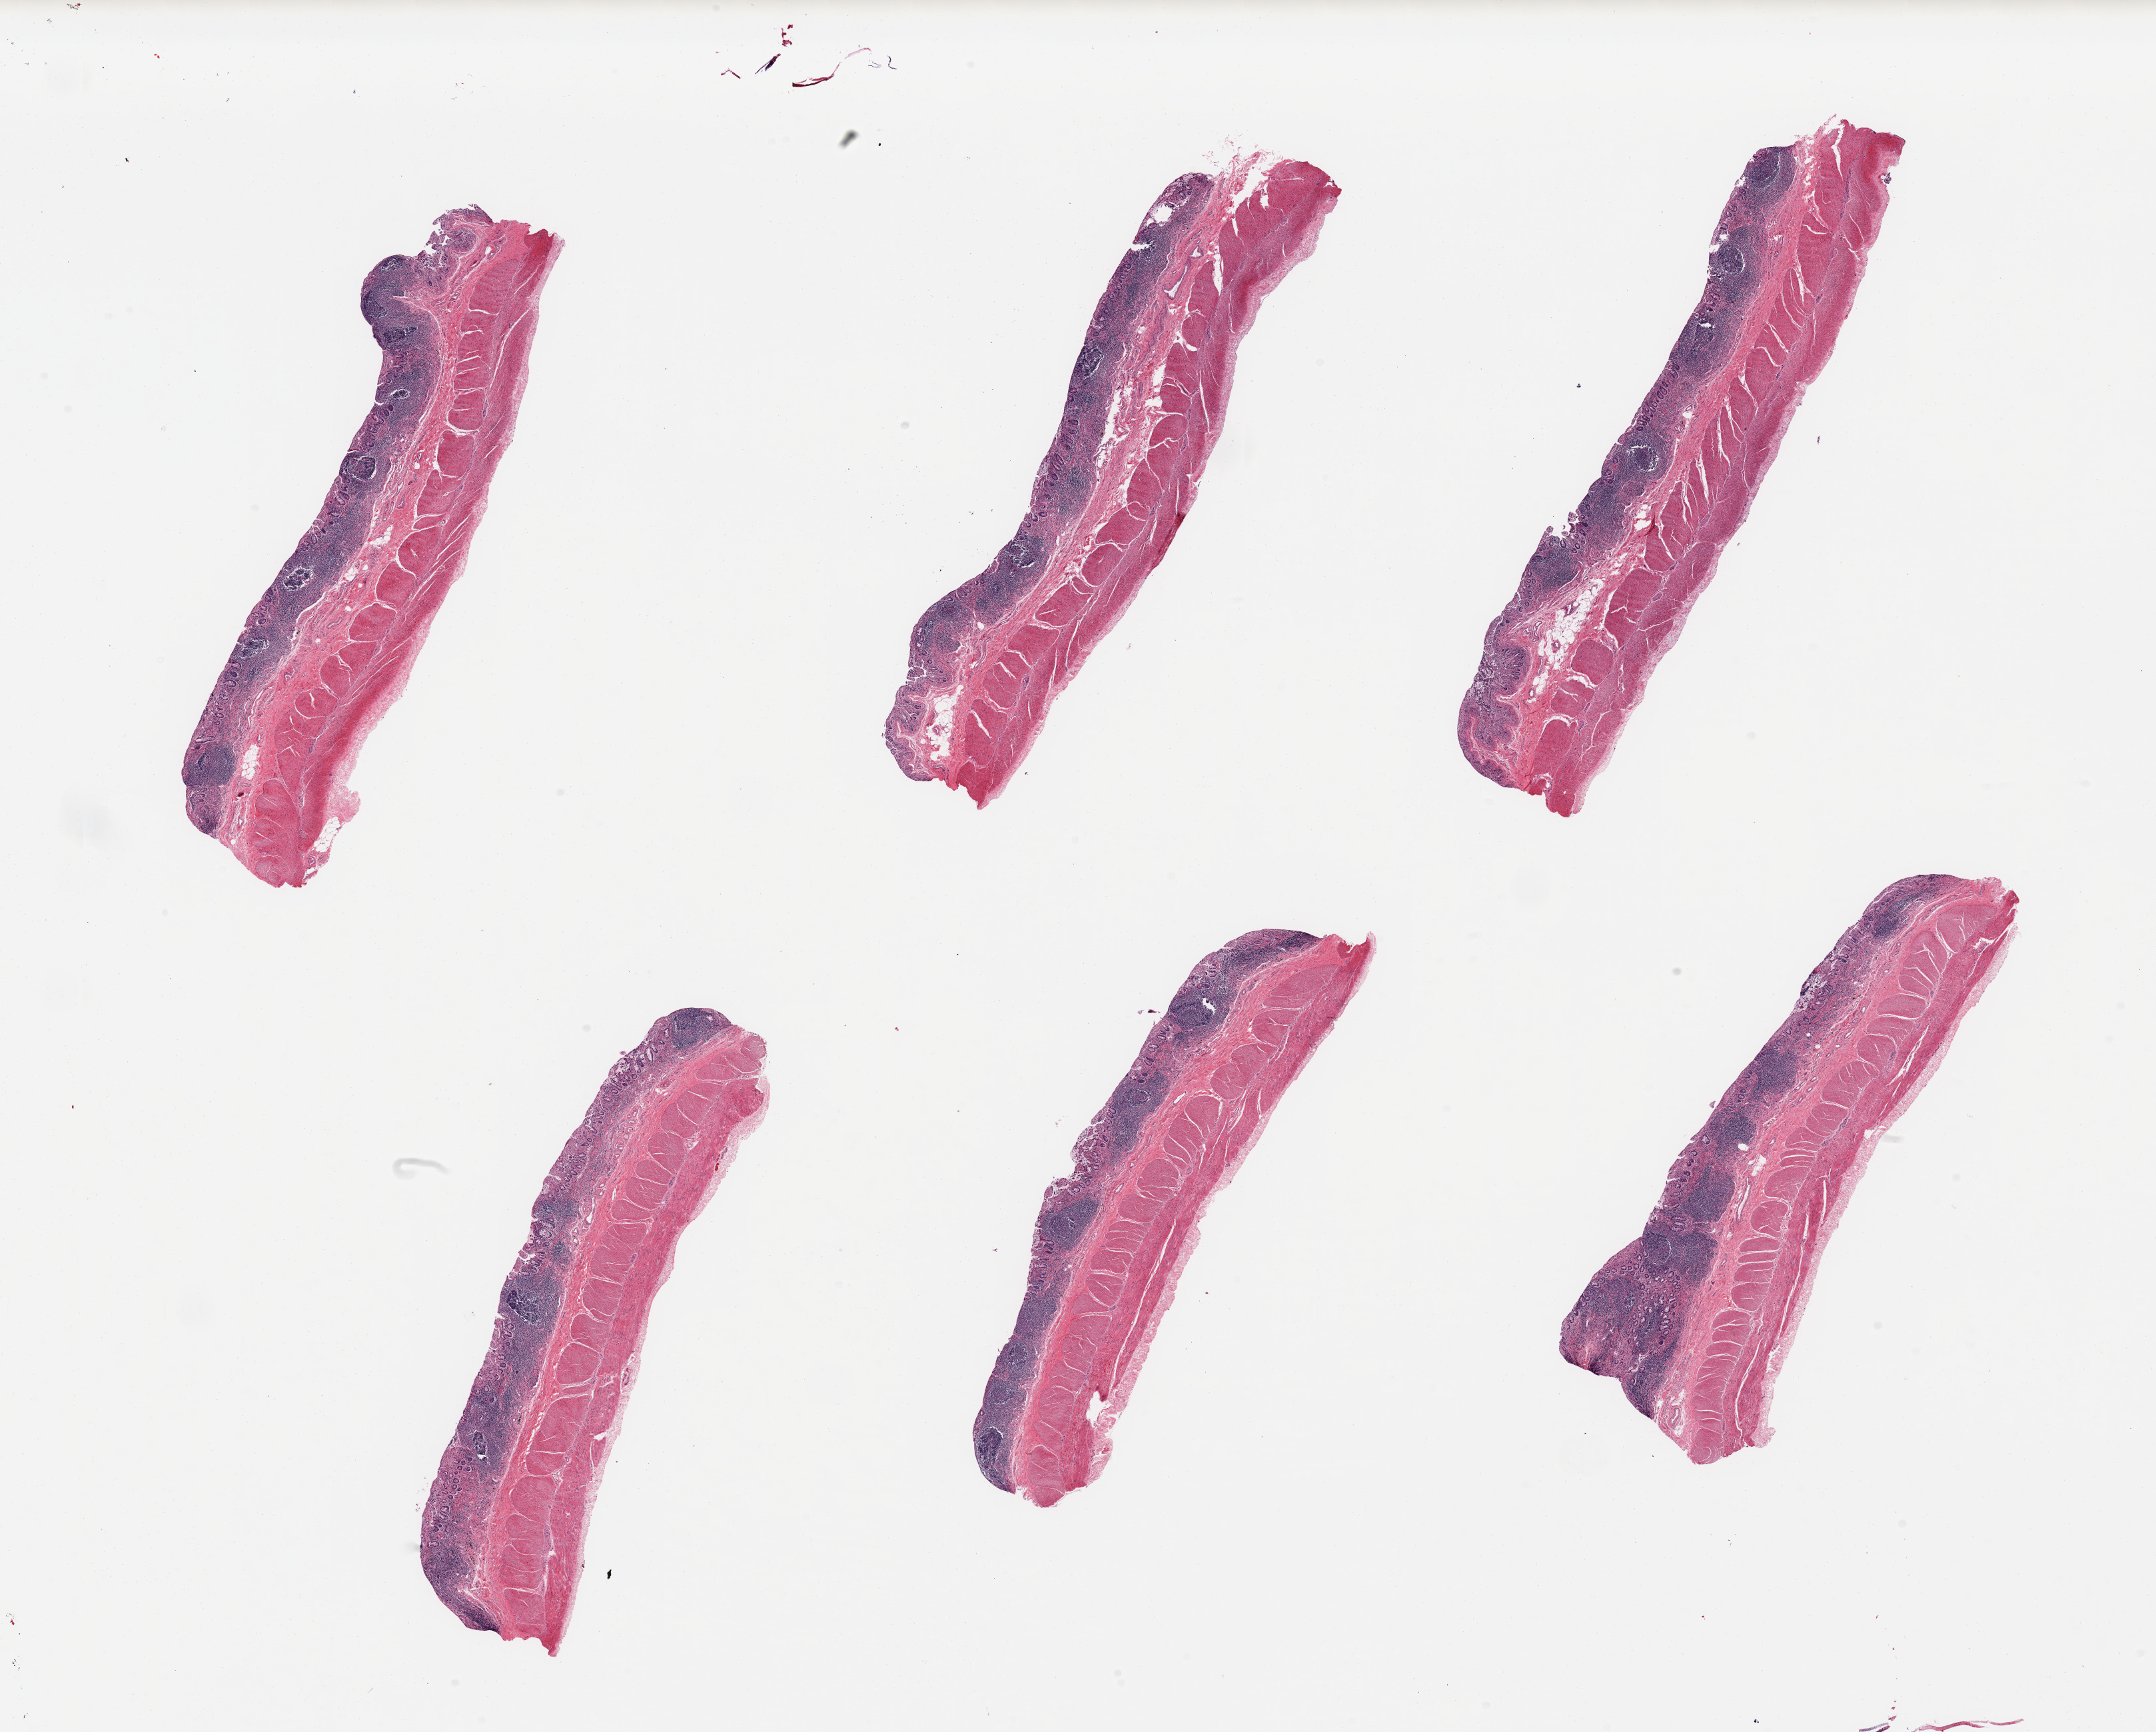
Digitized haematoxylin and eosin-stained section, brightfield, low-resolution overview of the scanned area, about 25.6 x 20.6 mm (acquisition: 20x scan). PAXgene-fixed, paraffin-embedded tissue. Target tissue: ileum. Tissue donor sample. Donor sex: male.
Pathologist's review note for this sample: 6 pieces, ~30% target lymphoid aggregates; glandular elements of mucosa largely autolyzed.